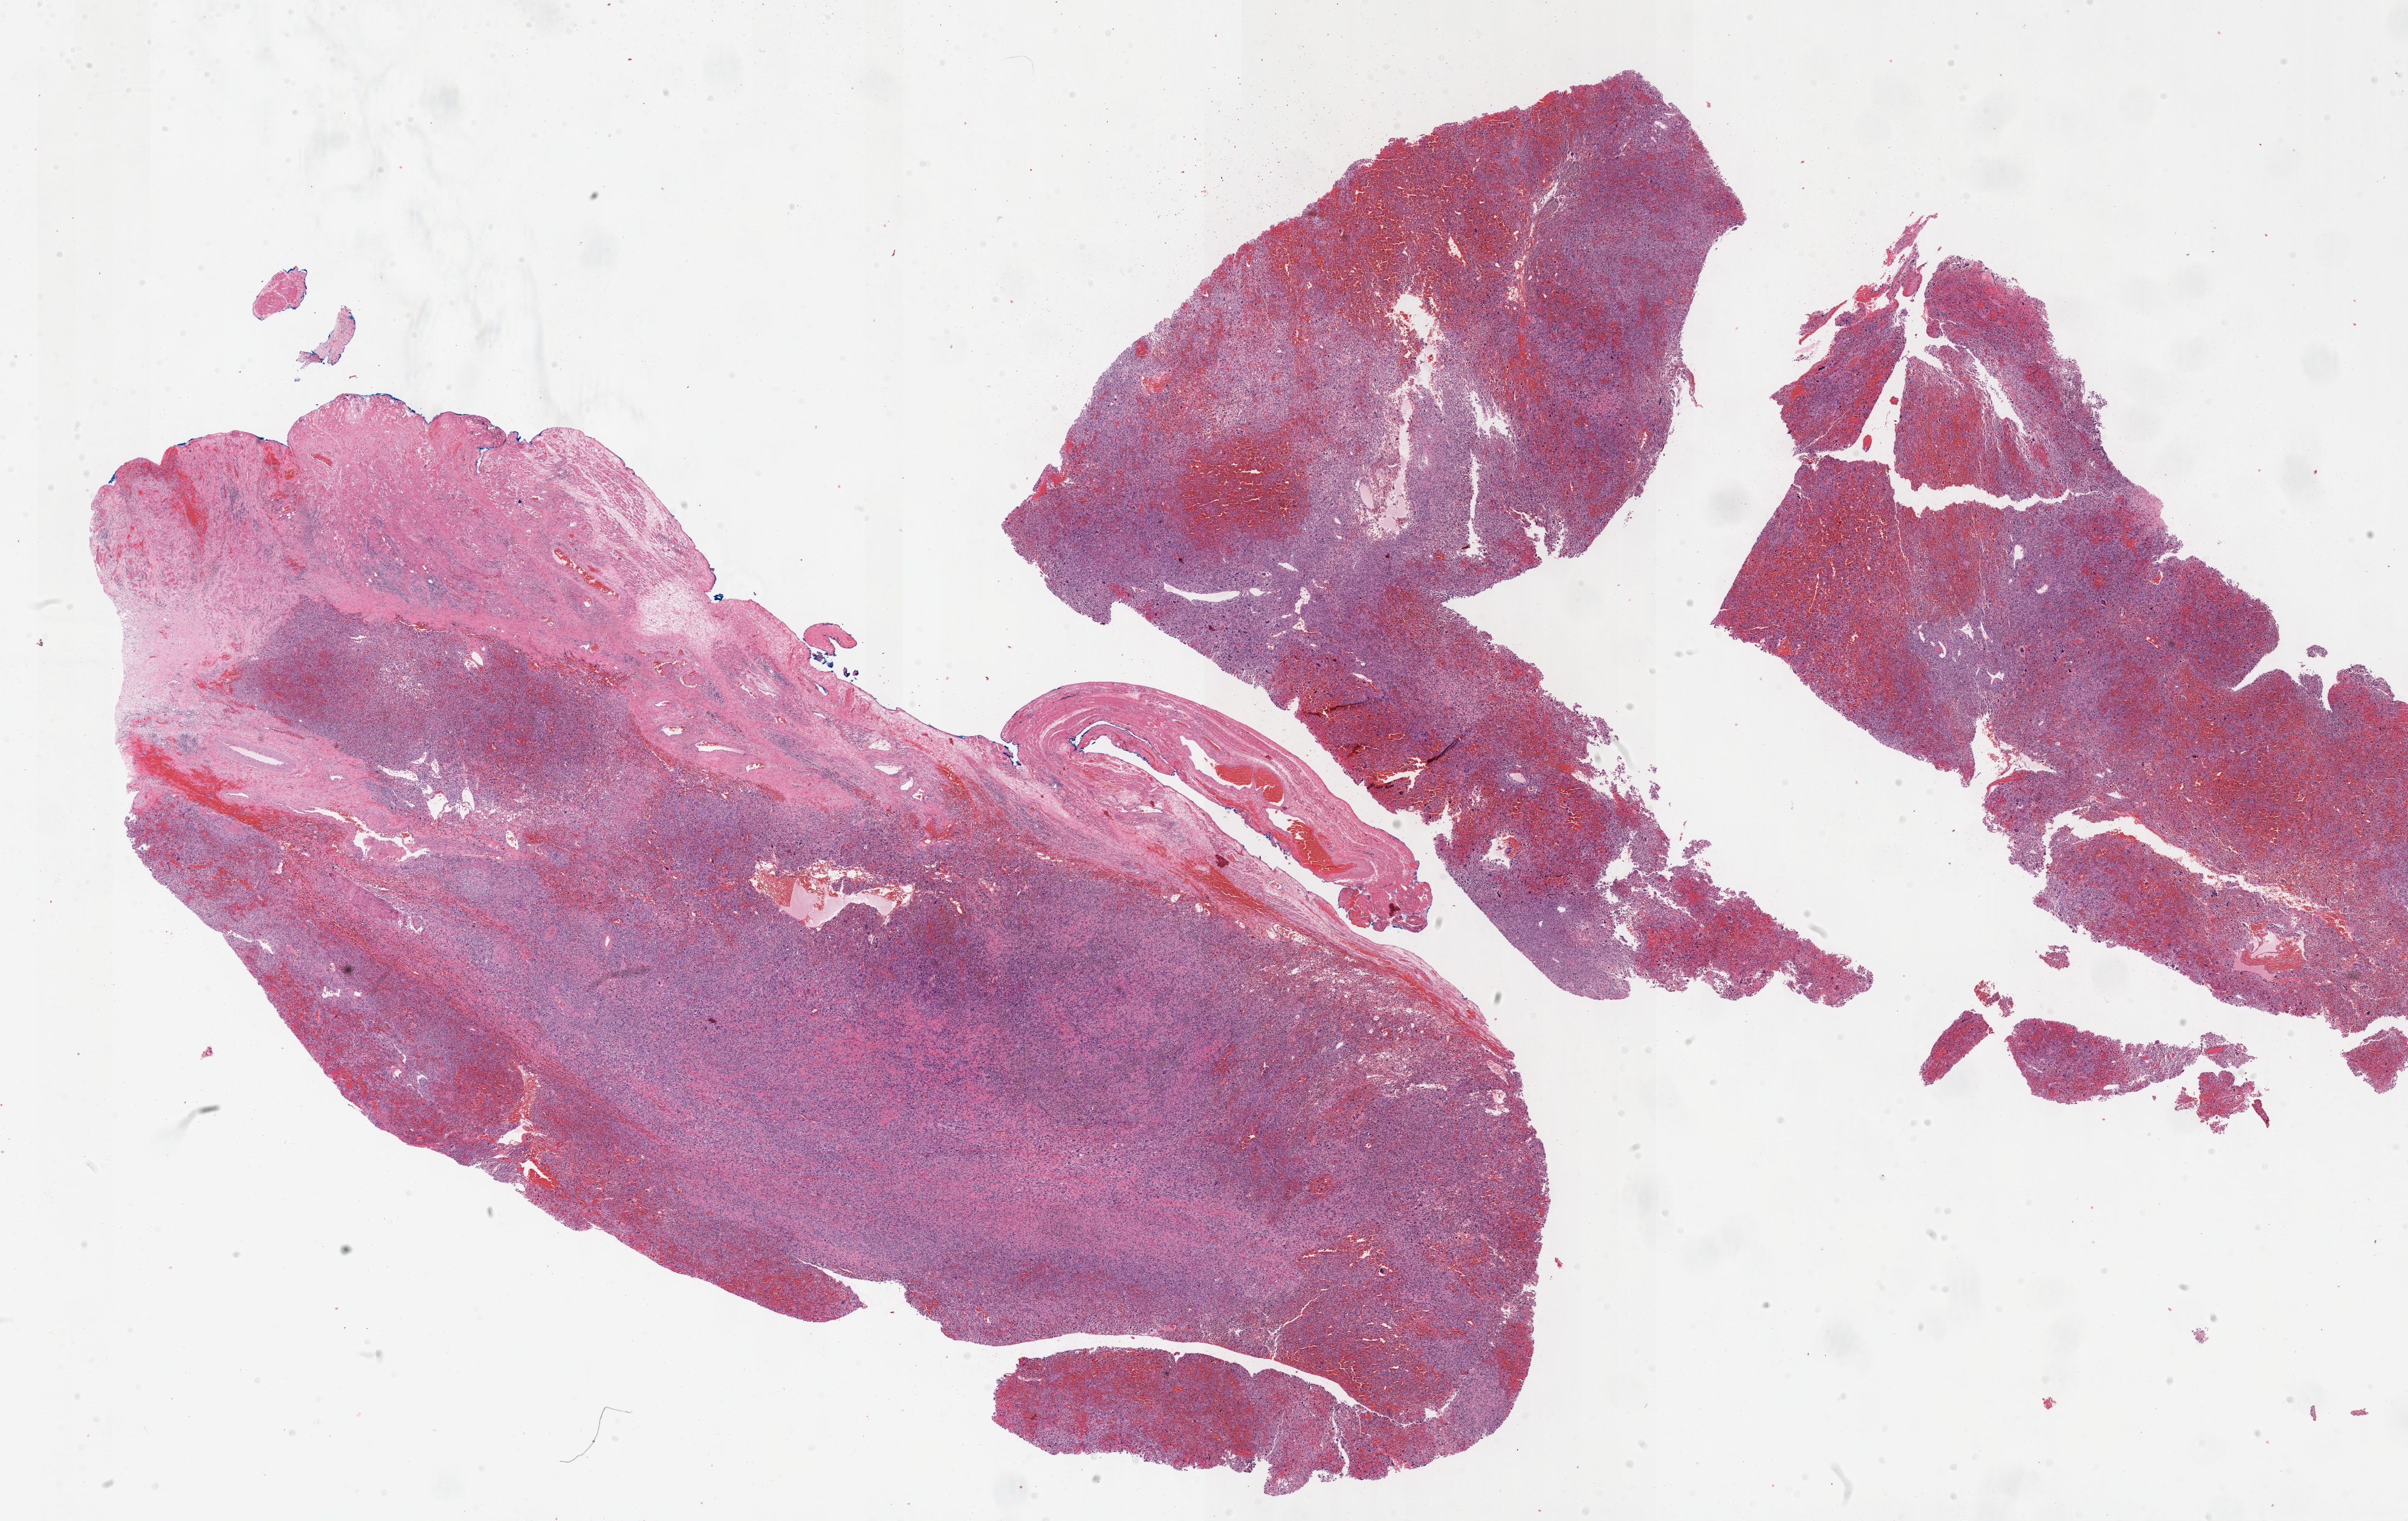
Whole-slide histology image, Hematoxylin and eosin (H&E) stained, whole scanned area (about 32.2 x 20.3 mm, slide scanned at 40x) shown as a low-resolution overview. Formalin-fixed paraffin-embedded (FFPE) diagnostic section. Connective, subcutaneous and other soft tissues, primary tumour sample. Male patient; age at initial diagnosis 56 years.
Histologic diagnosis: Undifferentiated sarcoma (connective, subcutaneous and other soft tissues of lower limb and hip).